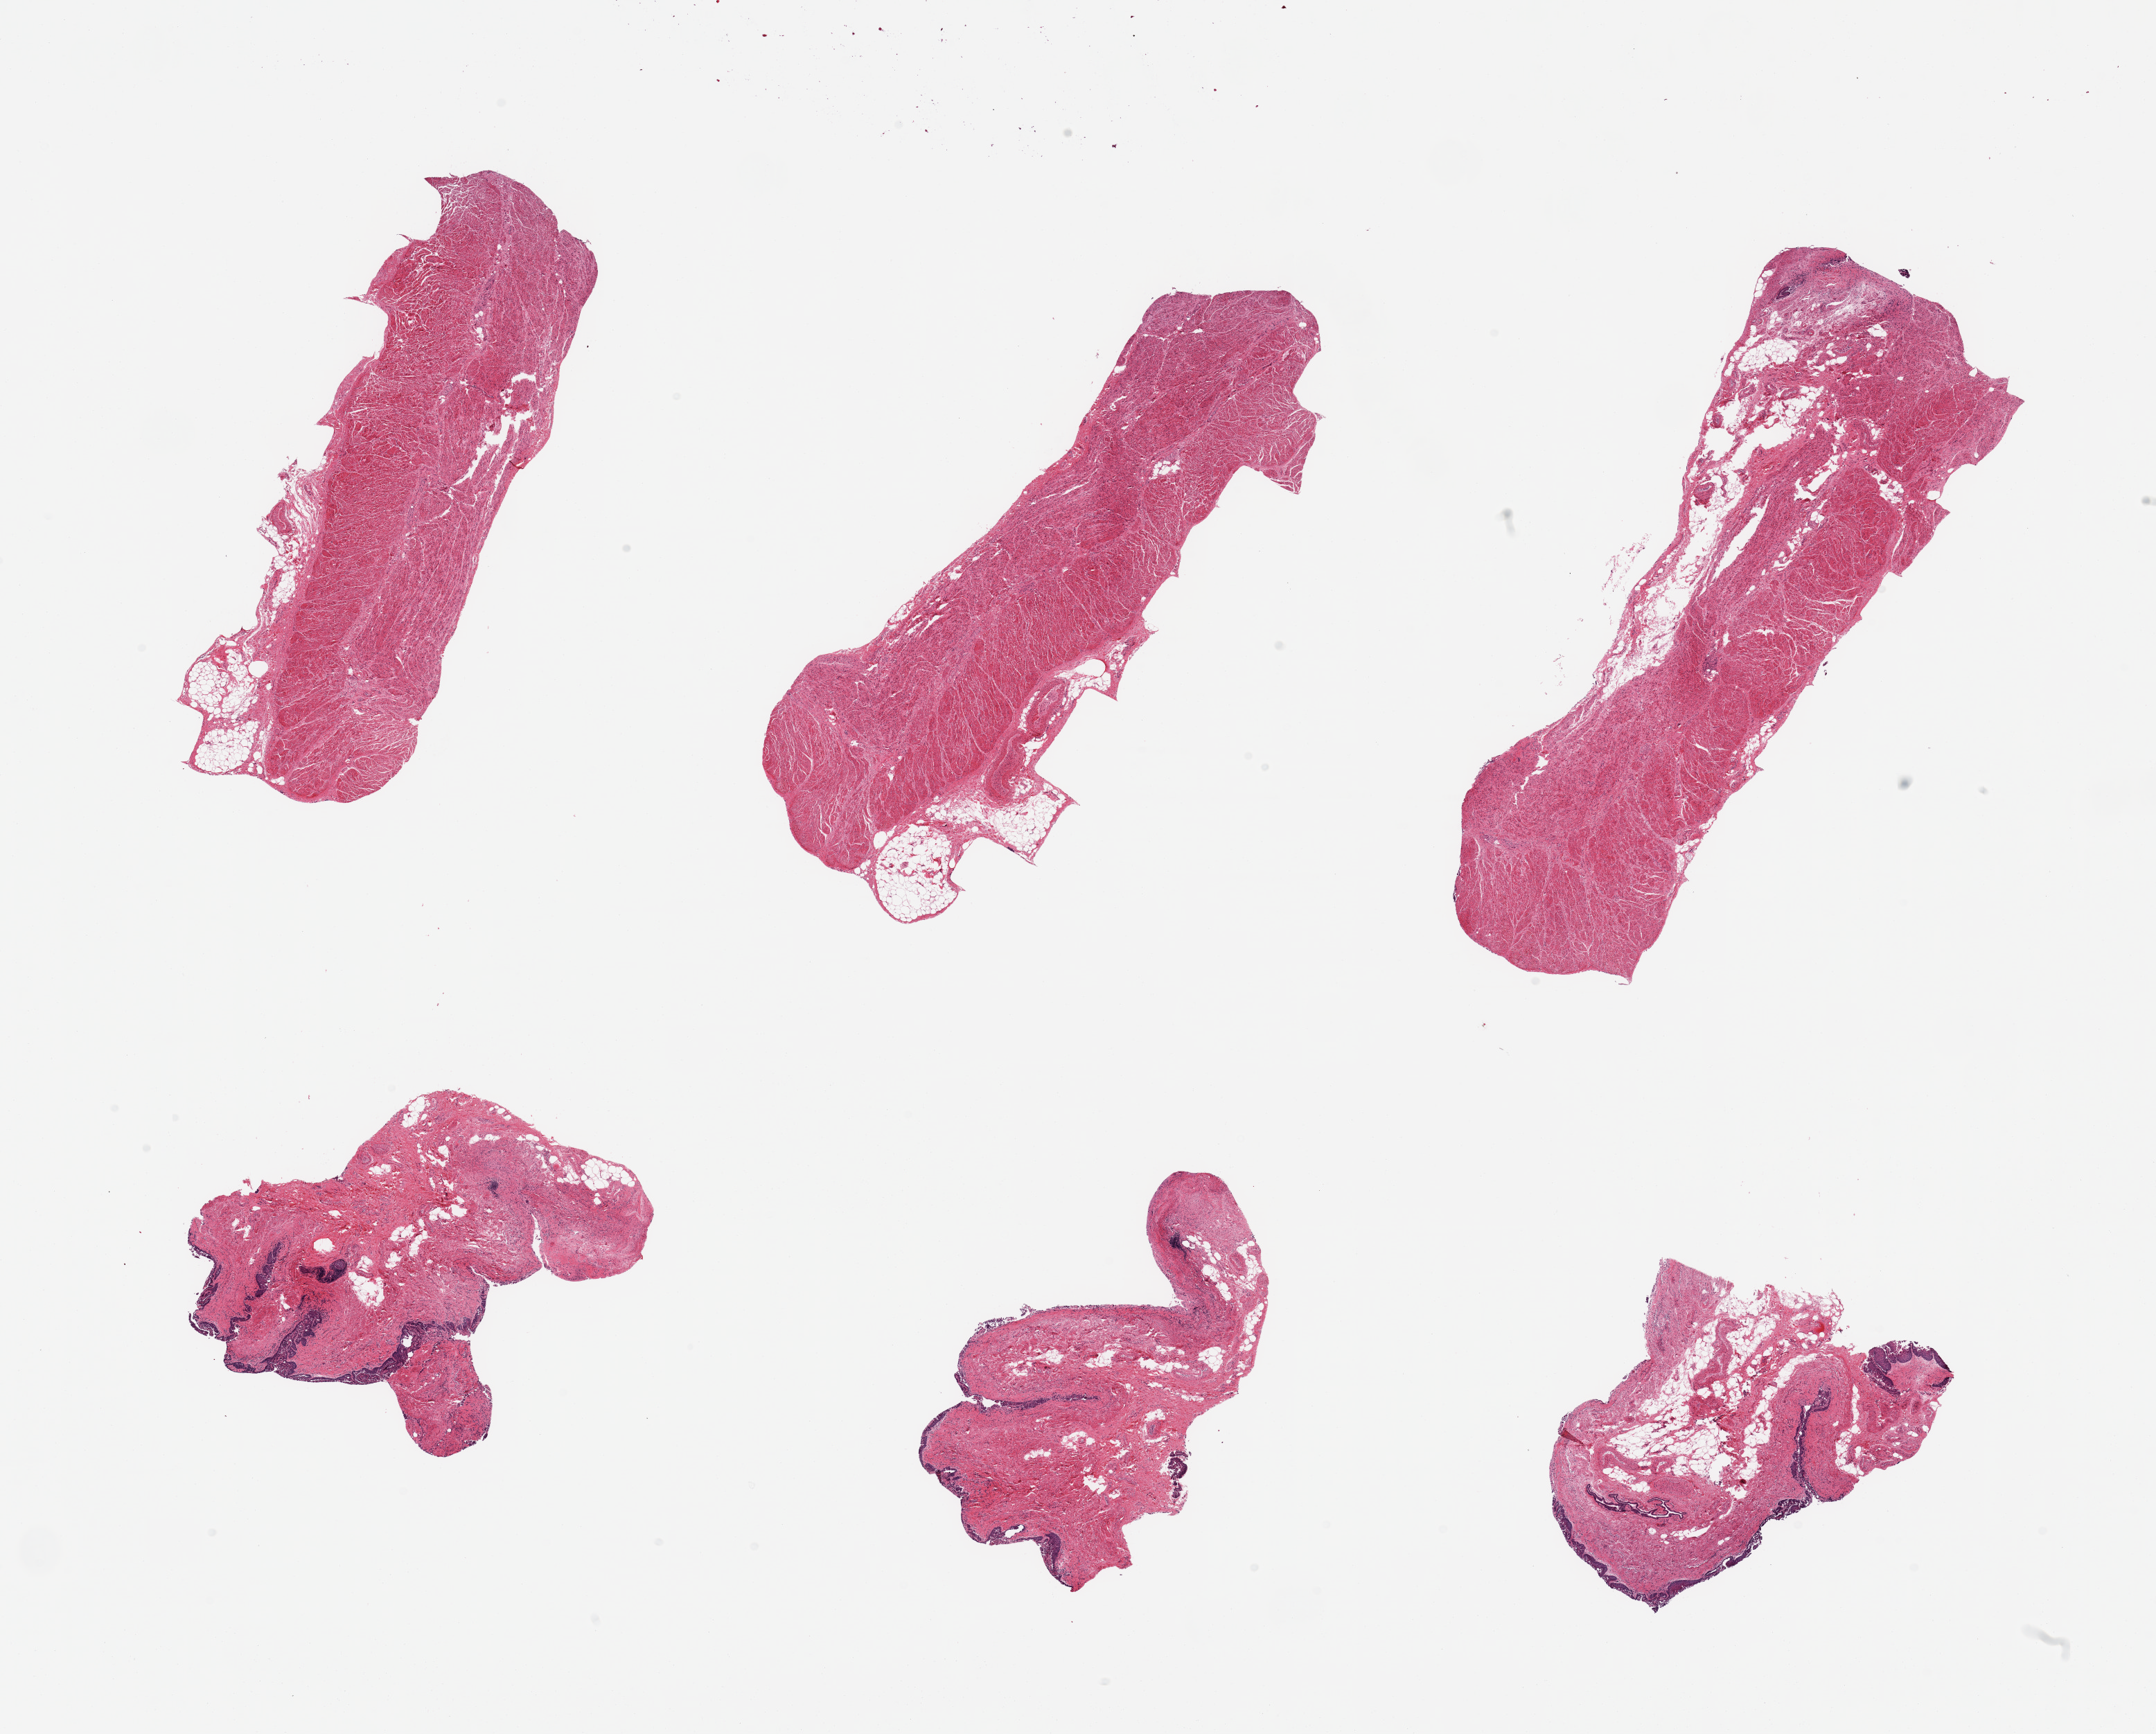
Whole-slide image, H&E stain, a low-resolution overview of the entire scanned area, about 24.6 x 19.8 mm (from a 20x scan). PAXgene-fixed paraffin-embedded (PFPE) section. Sampled site (target tissue): gastroesophageal junction. Donor tissue sample. Male donor.
Reviewer comment on this tissue sample: 6 pieces; 3 are muscularis, 3 are mucosa (not target).